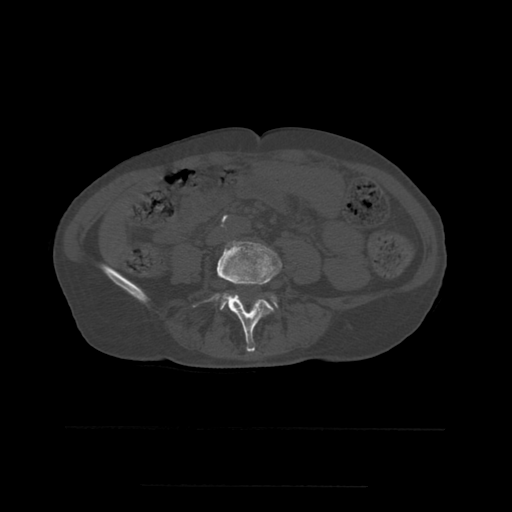
CT including the spine, one axial slice. Position 162 of 544 along the scan axis. Bone window (W 1800 / L 400 HU). 1.25 mm slice thickness. 512 × 512 image matrix. Patient age 58 years. Case-level facts recorded for this patient, not image findings: primary cancer: lung.
Annotated regions visible in this slice (semi-automatic segmentation, software-assisted and operator-edited):
- L4 vertebra: bounding box (x1, y1, x2, y2) in pixels: (193, 242, 282, 352)
- L5 vertebra: (220, 293, 278, 310)